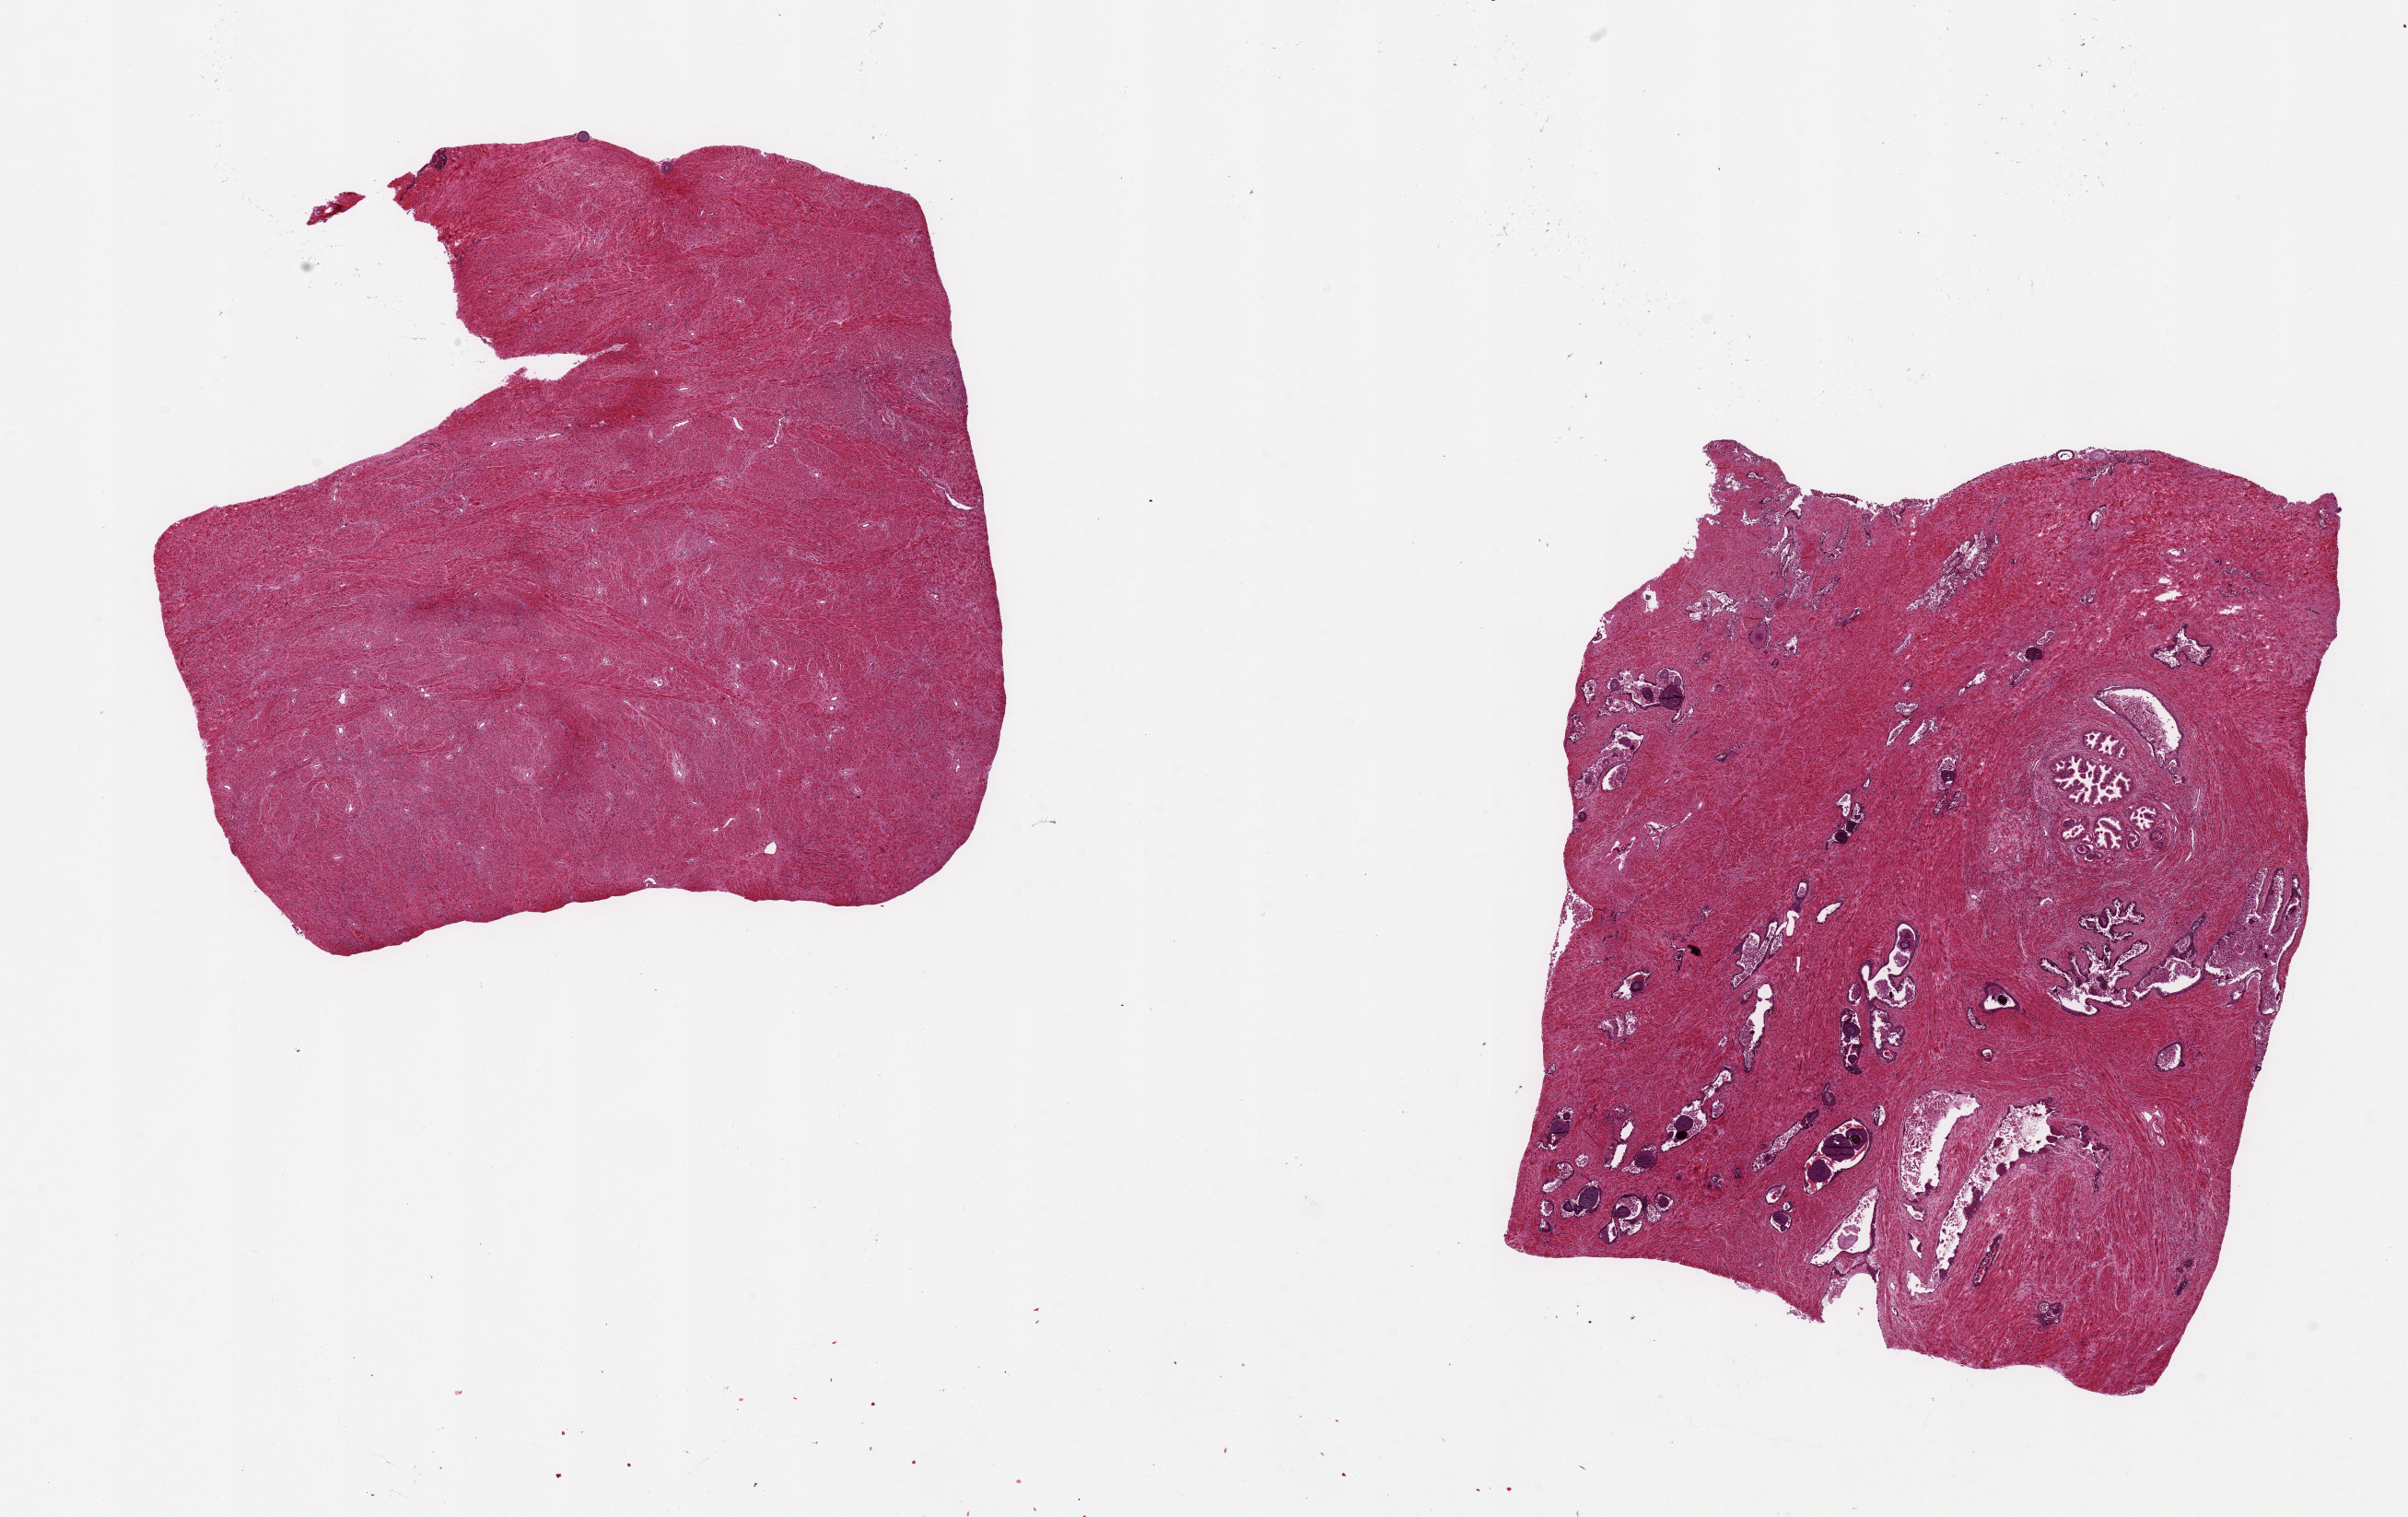
Digitized H&E-stained section — low-resolution overview of the scanned area, about 20.7 x 13.0 mm (acquisition: 20x scan). PAXgene-fixed, paraffin-embedded tissue. Section of prostate (target tissue). Donor tissue sample. Donor sex: male.
Review note (as recorded): 2 pieces, one aliqout is all stroma. ~7x6mm.